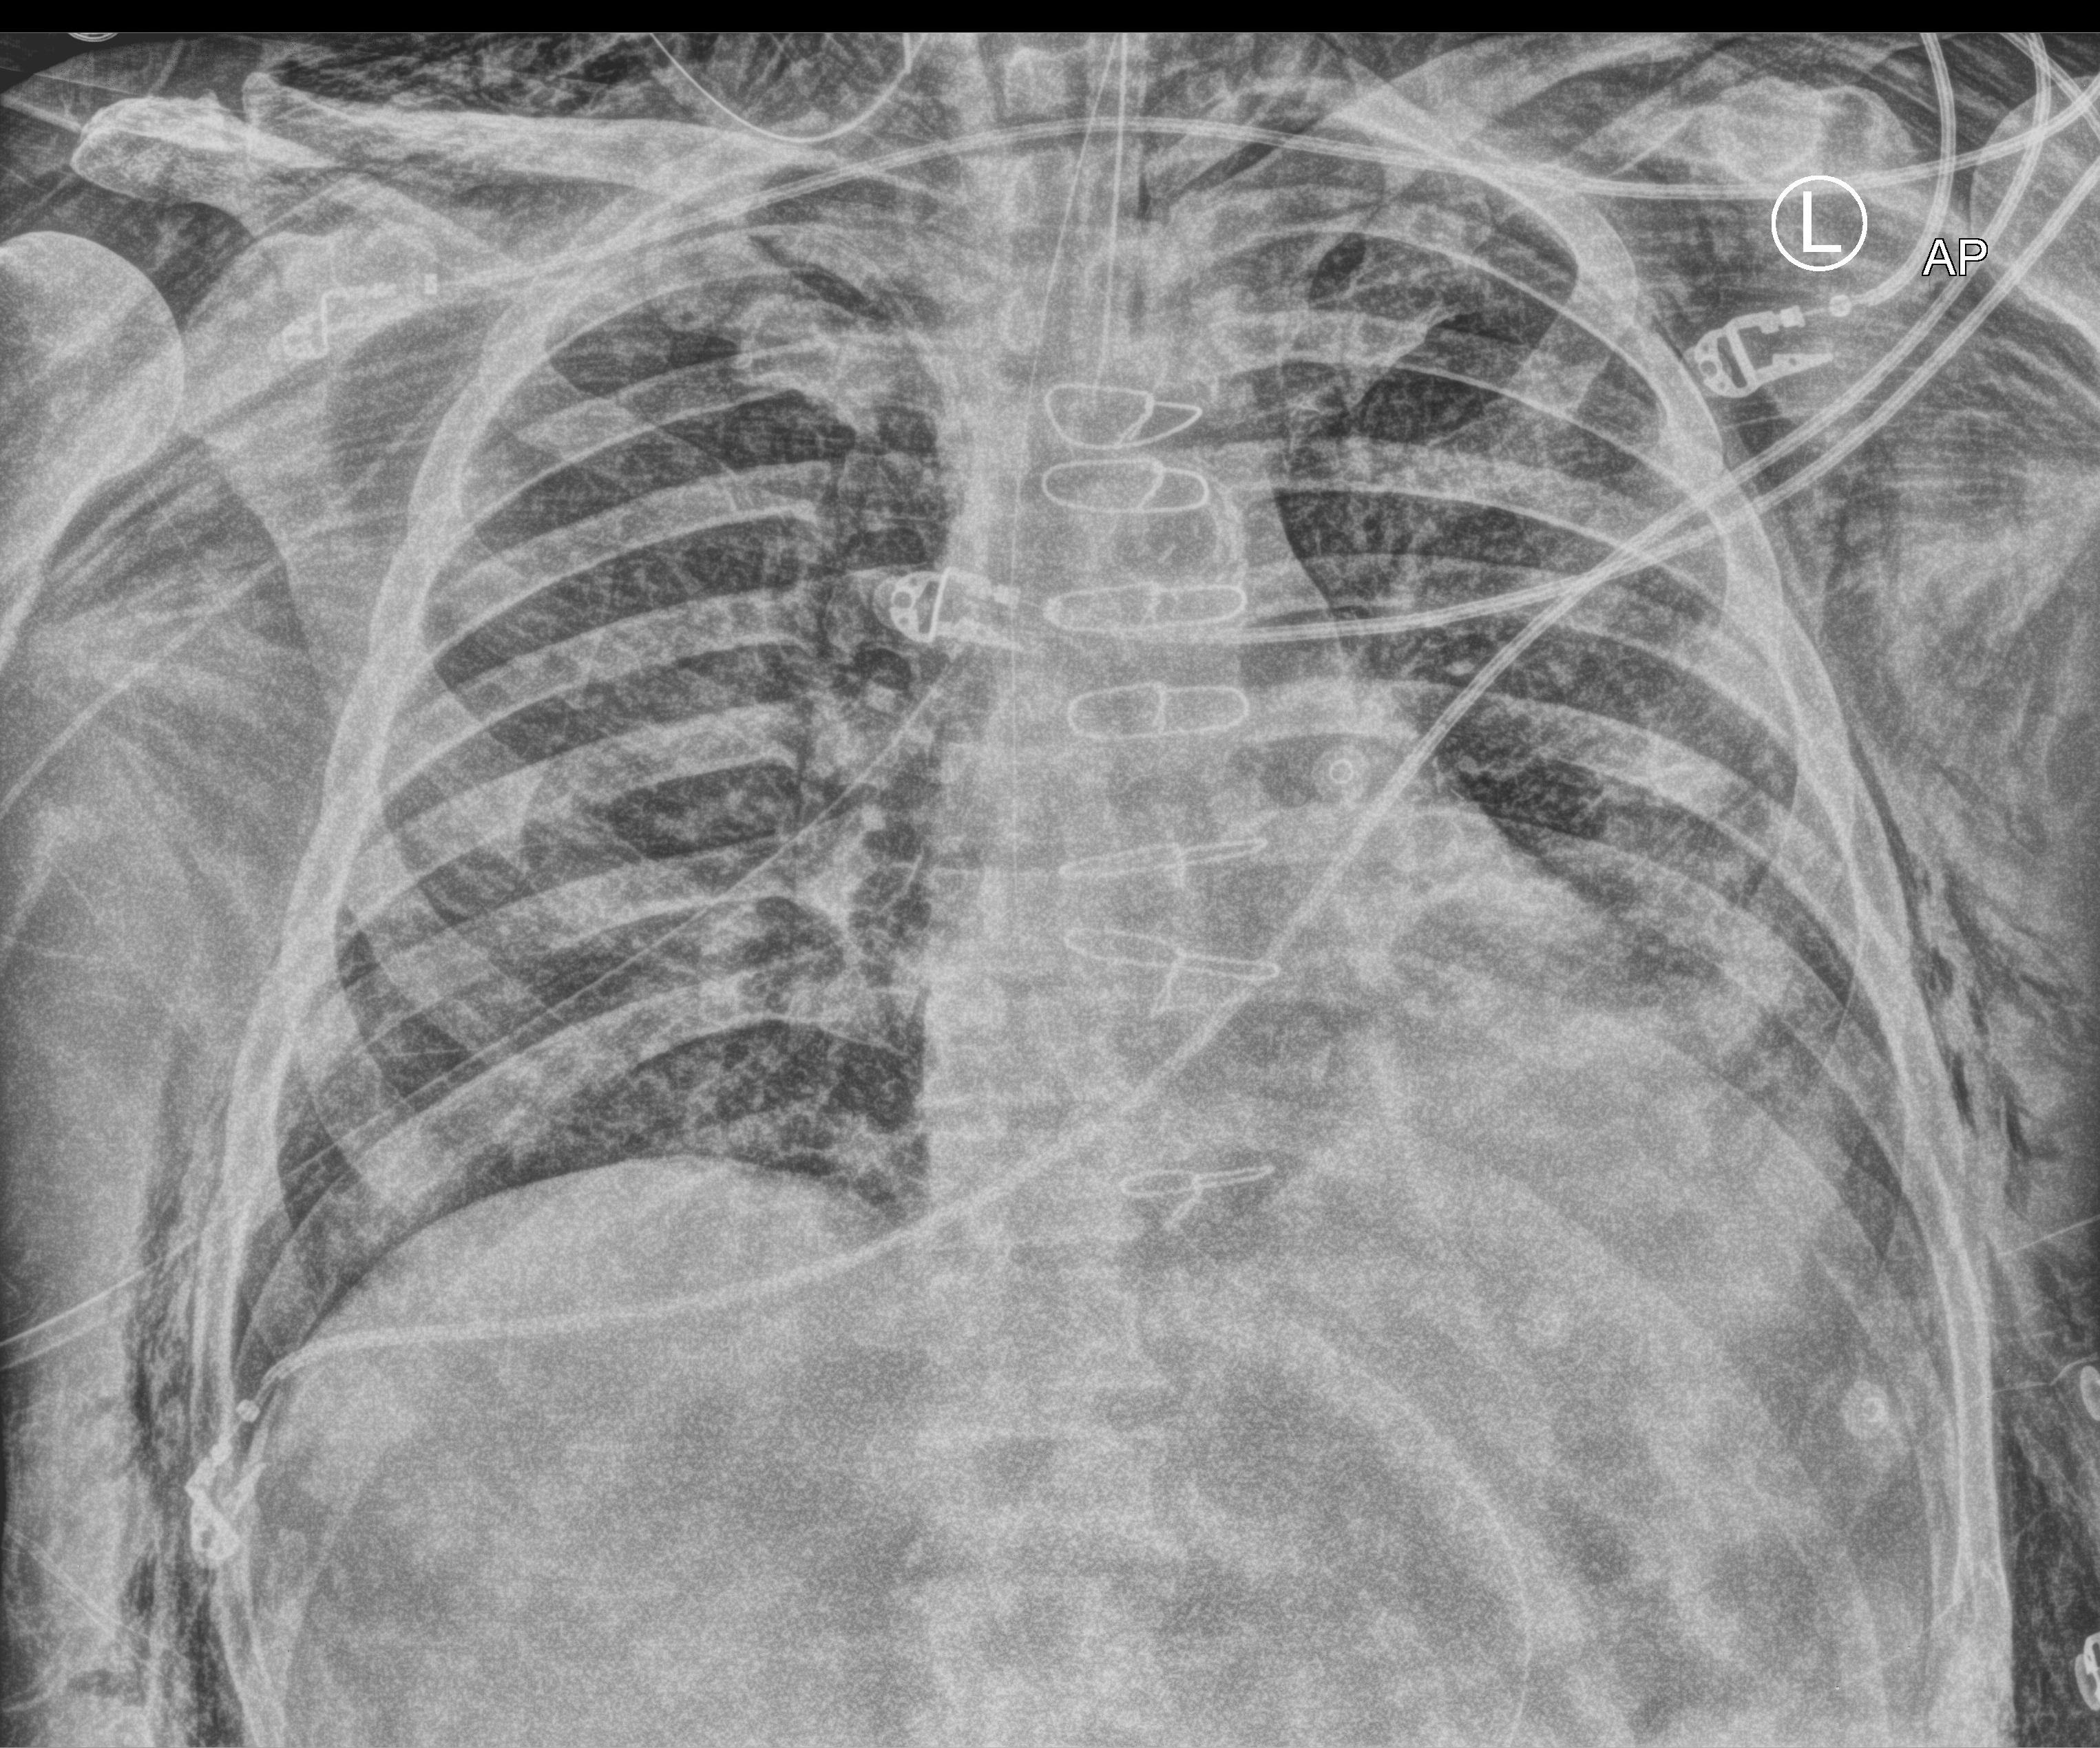
Bedside chest radiograph (computed radiography). Male patient hospitalised with COVID-19, age 60–74 years.
Admission-level facts for this patient (not findings on this image; timing relative to this image not recorded):
- mechanically ventilated during this hospital stay: yes
- length of hospital stay: 44 days